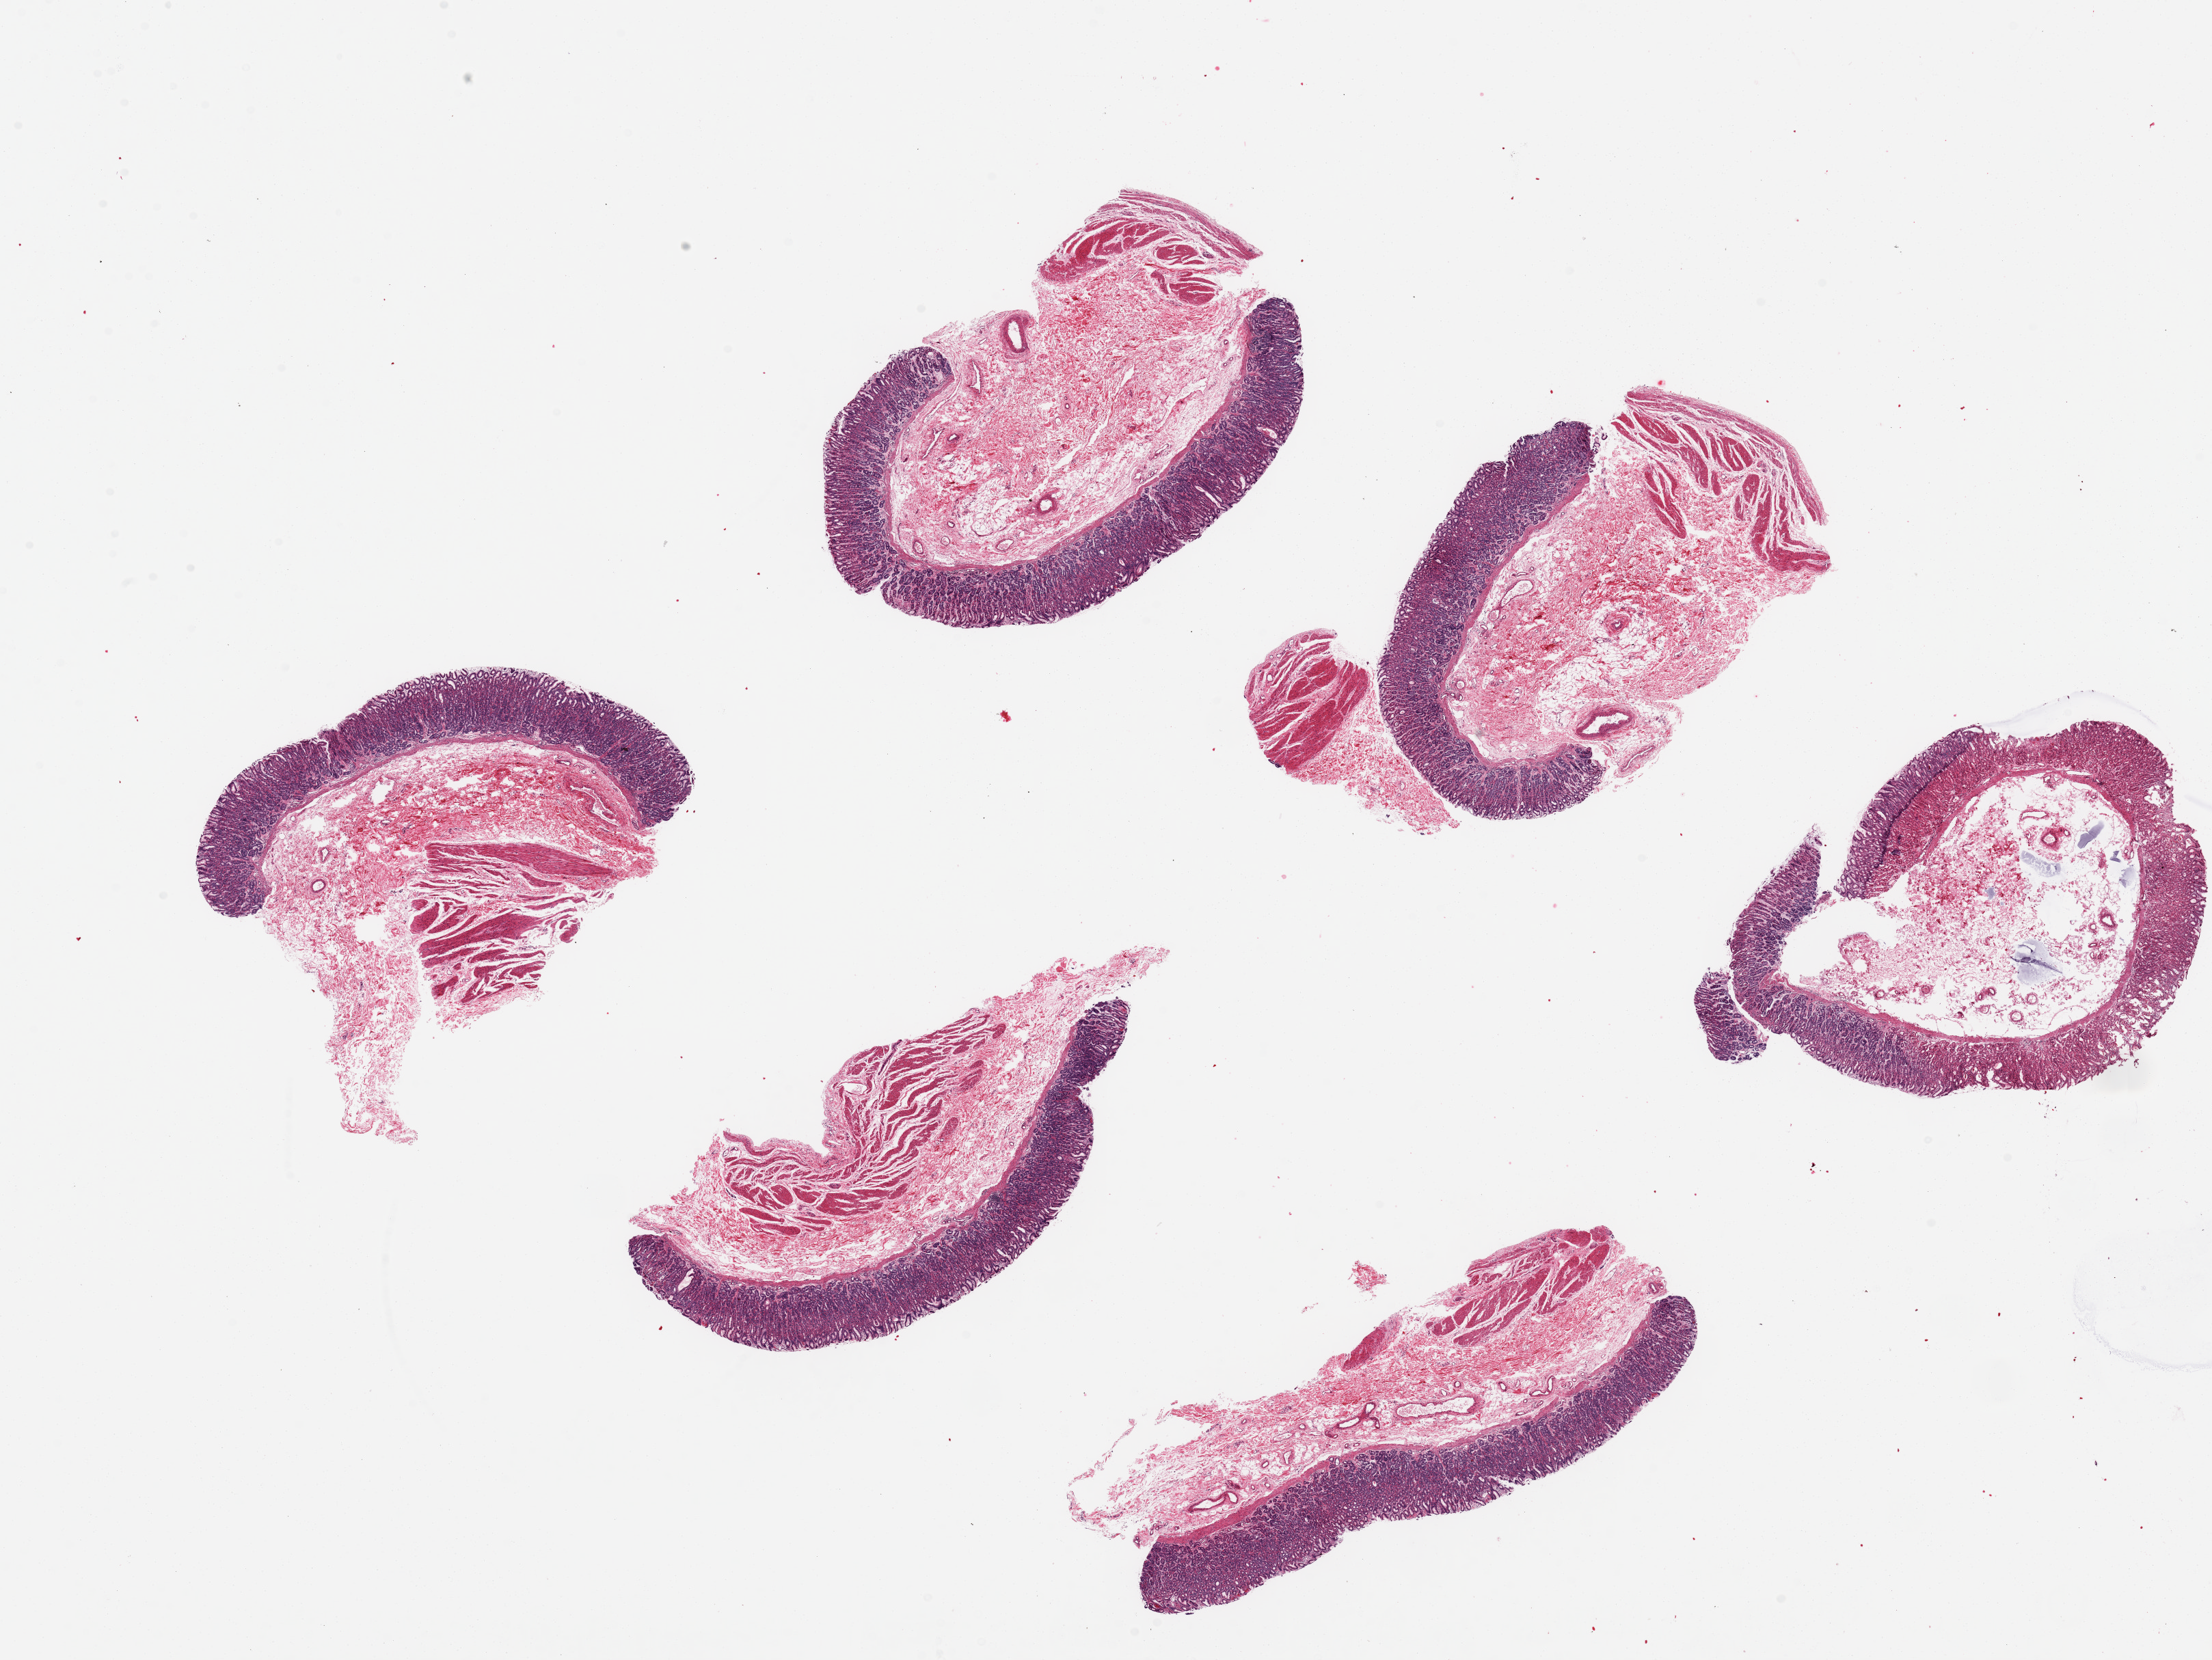
Digitized H&E-stained section — whole scanned area (about 25.6 x 19.2 mm, slide scanned at 20x) shown as a low-resolution overview. PAXgene-fixed, paraffin-embedded tissue. Target tissue: stomach. Tissue donor sample. Female donor.
Review note (as recorded): 6 pieces, one not well stained/preserved; mucosa 0.8 mm; ~7x3mm.